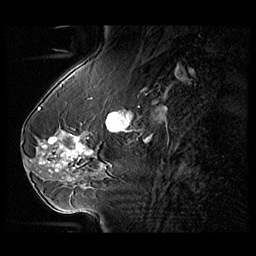
Breast MRI (dynamic contrast-enhanced), one sagittal slice. Slice 39 of 104 in the series (ordered by position). 3 images stored at this slice position (order not interpretable as contrast timing). 1.5 T. TE 1.3 ms, TR 5.5 ms. 256 × 256 image matrix. Patient: female, 54 years. Case-level facts recorded for this patient, not image findings: setting: breast cancer imaged before/during neoadjuvant chemotherapy; receptor status: HR-positive, HER2-negative.
Annotated regions visible in this slice (semi-automatic segmentation, software-assisted and operator-edited):
- analysis volume of interest (the breast-tissue region the enhancement analysis was run in; not a lesion): bounding box <28,127,104,182> (left, top, right, bottom; pixels)
- tumour enhancement mask (voxels above the 140 % enhancement threshold inside the analysis volume of interest): <39,137,92,172>